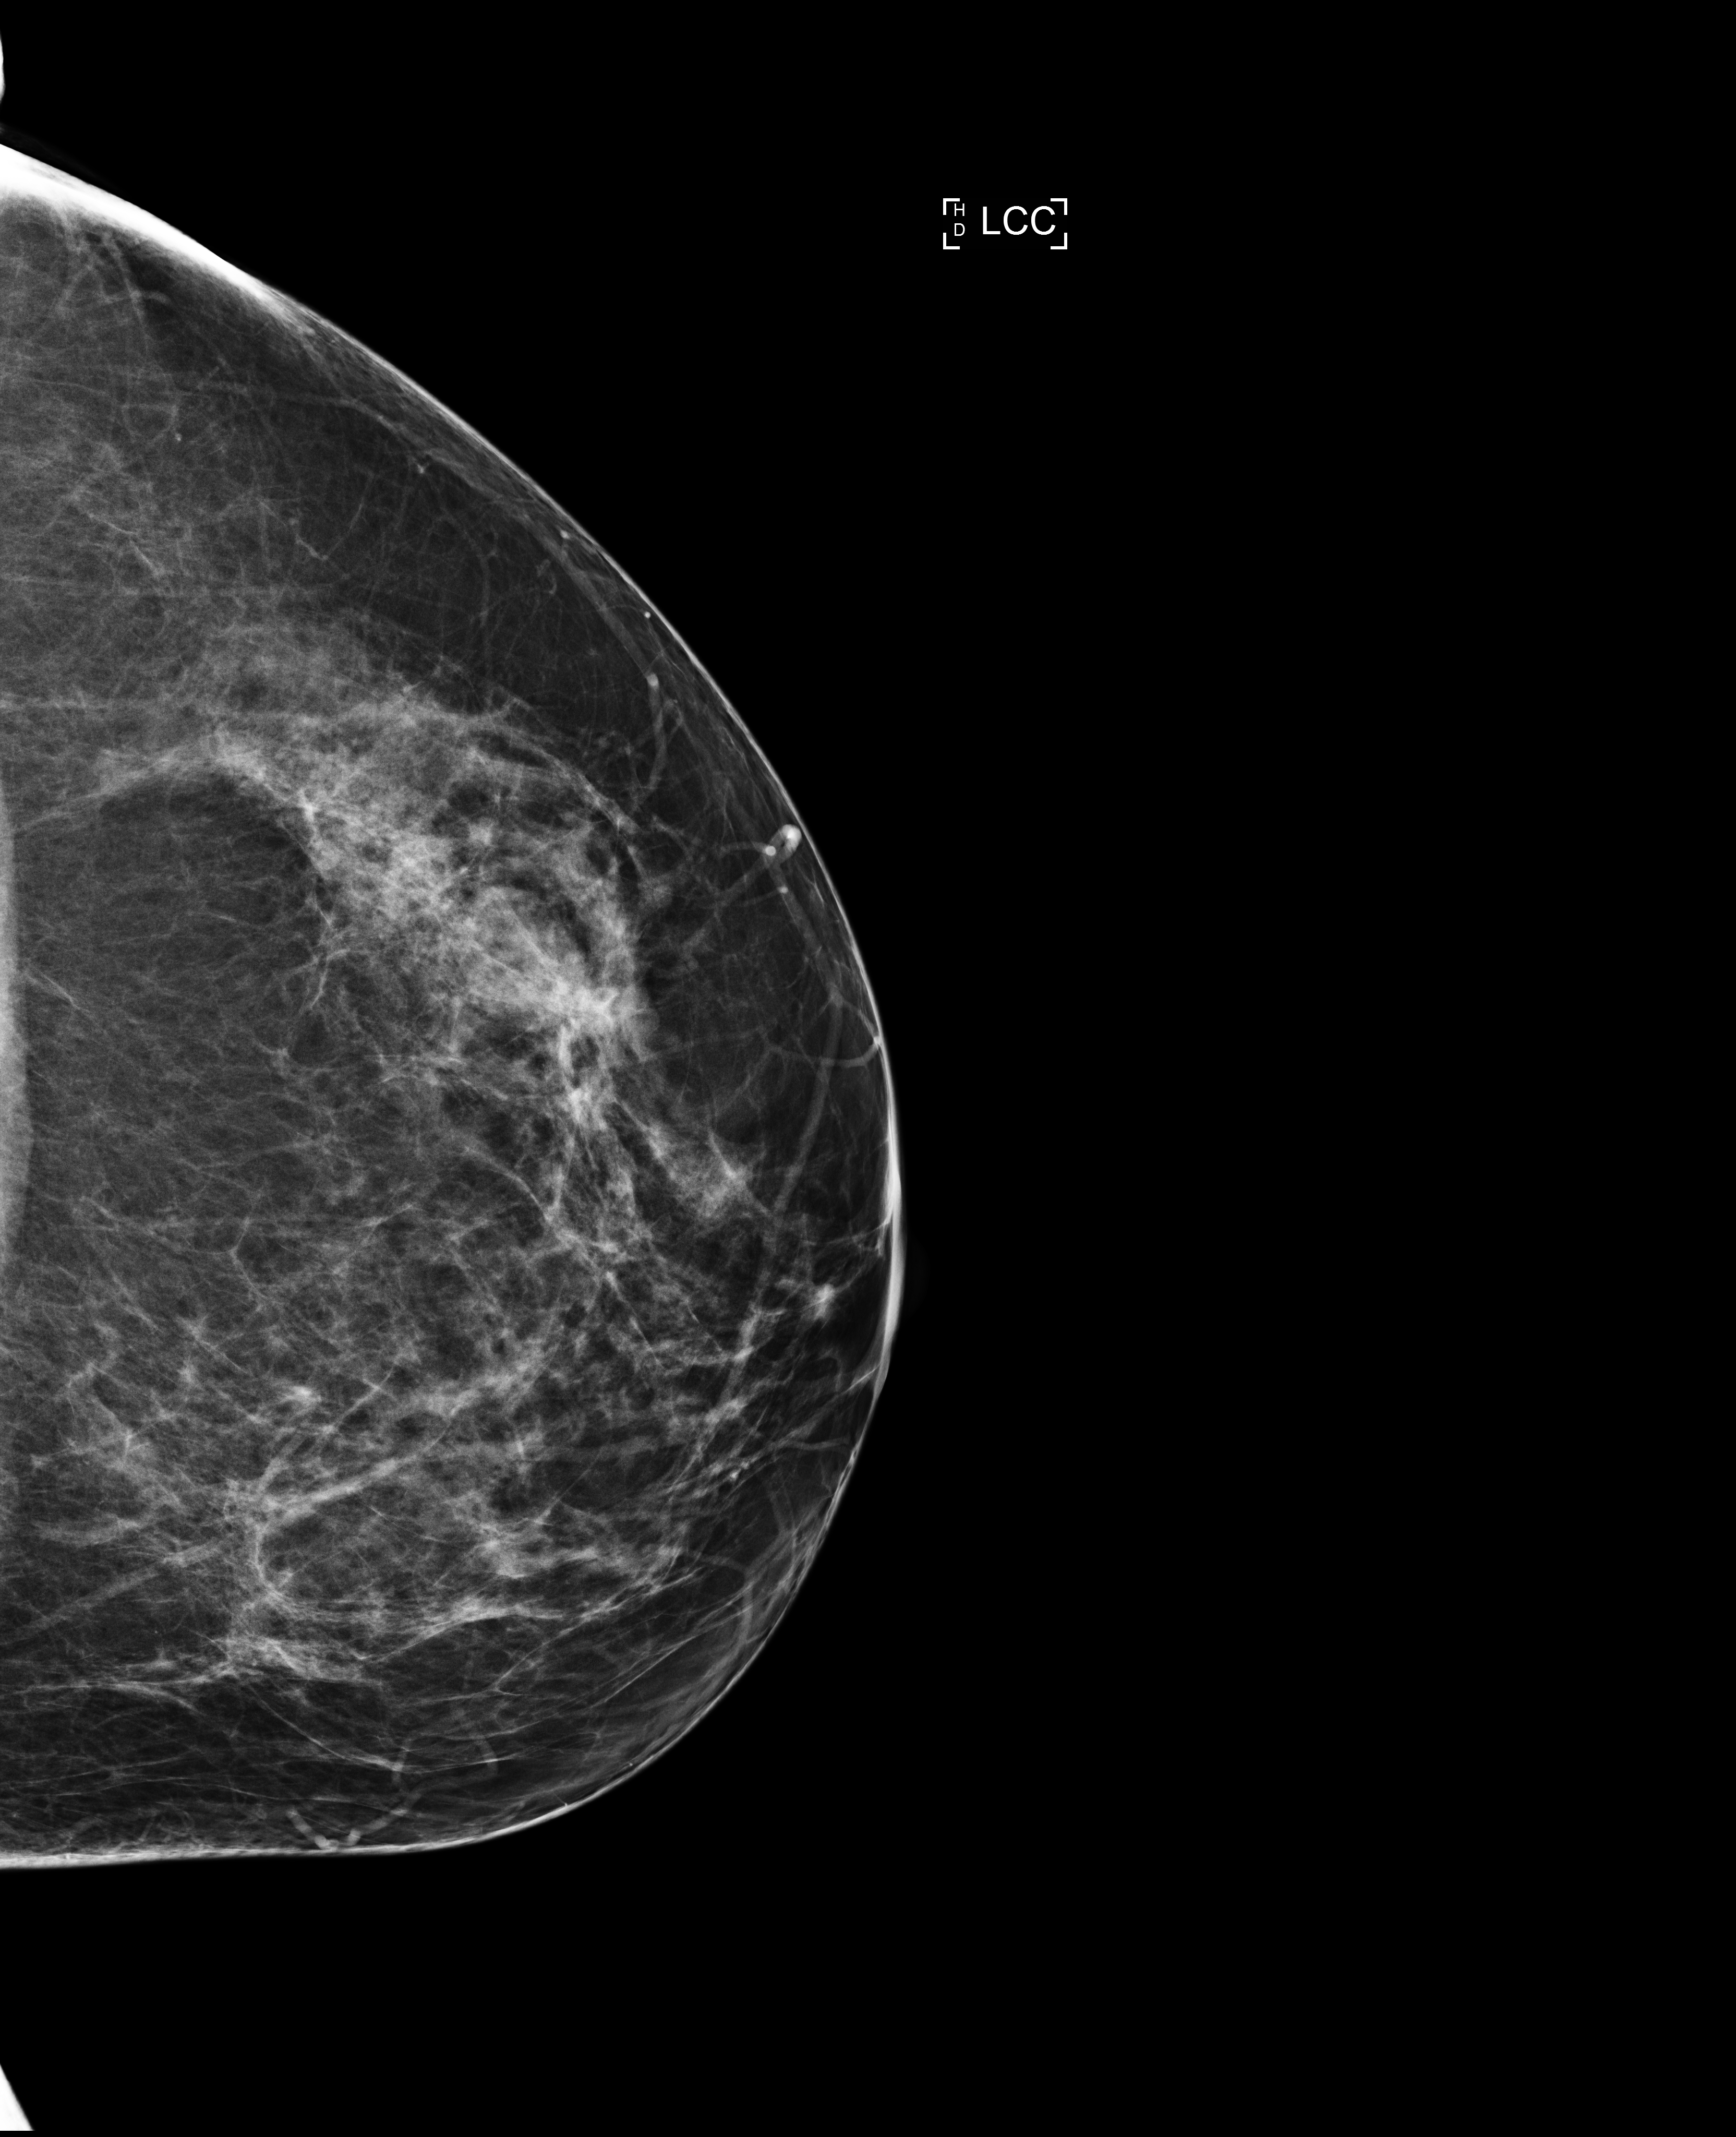
Annual screening mammography examination; compressed breast thickness 66 mm; system: Selenia Dimensions. Patient: female, 51 years.
Image type: full-field digital mammogram. Breast: left. Projection: CC view.